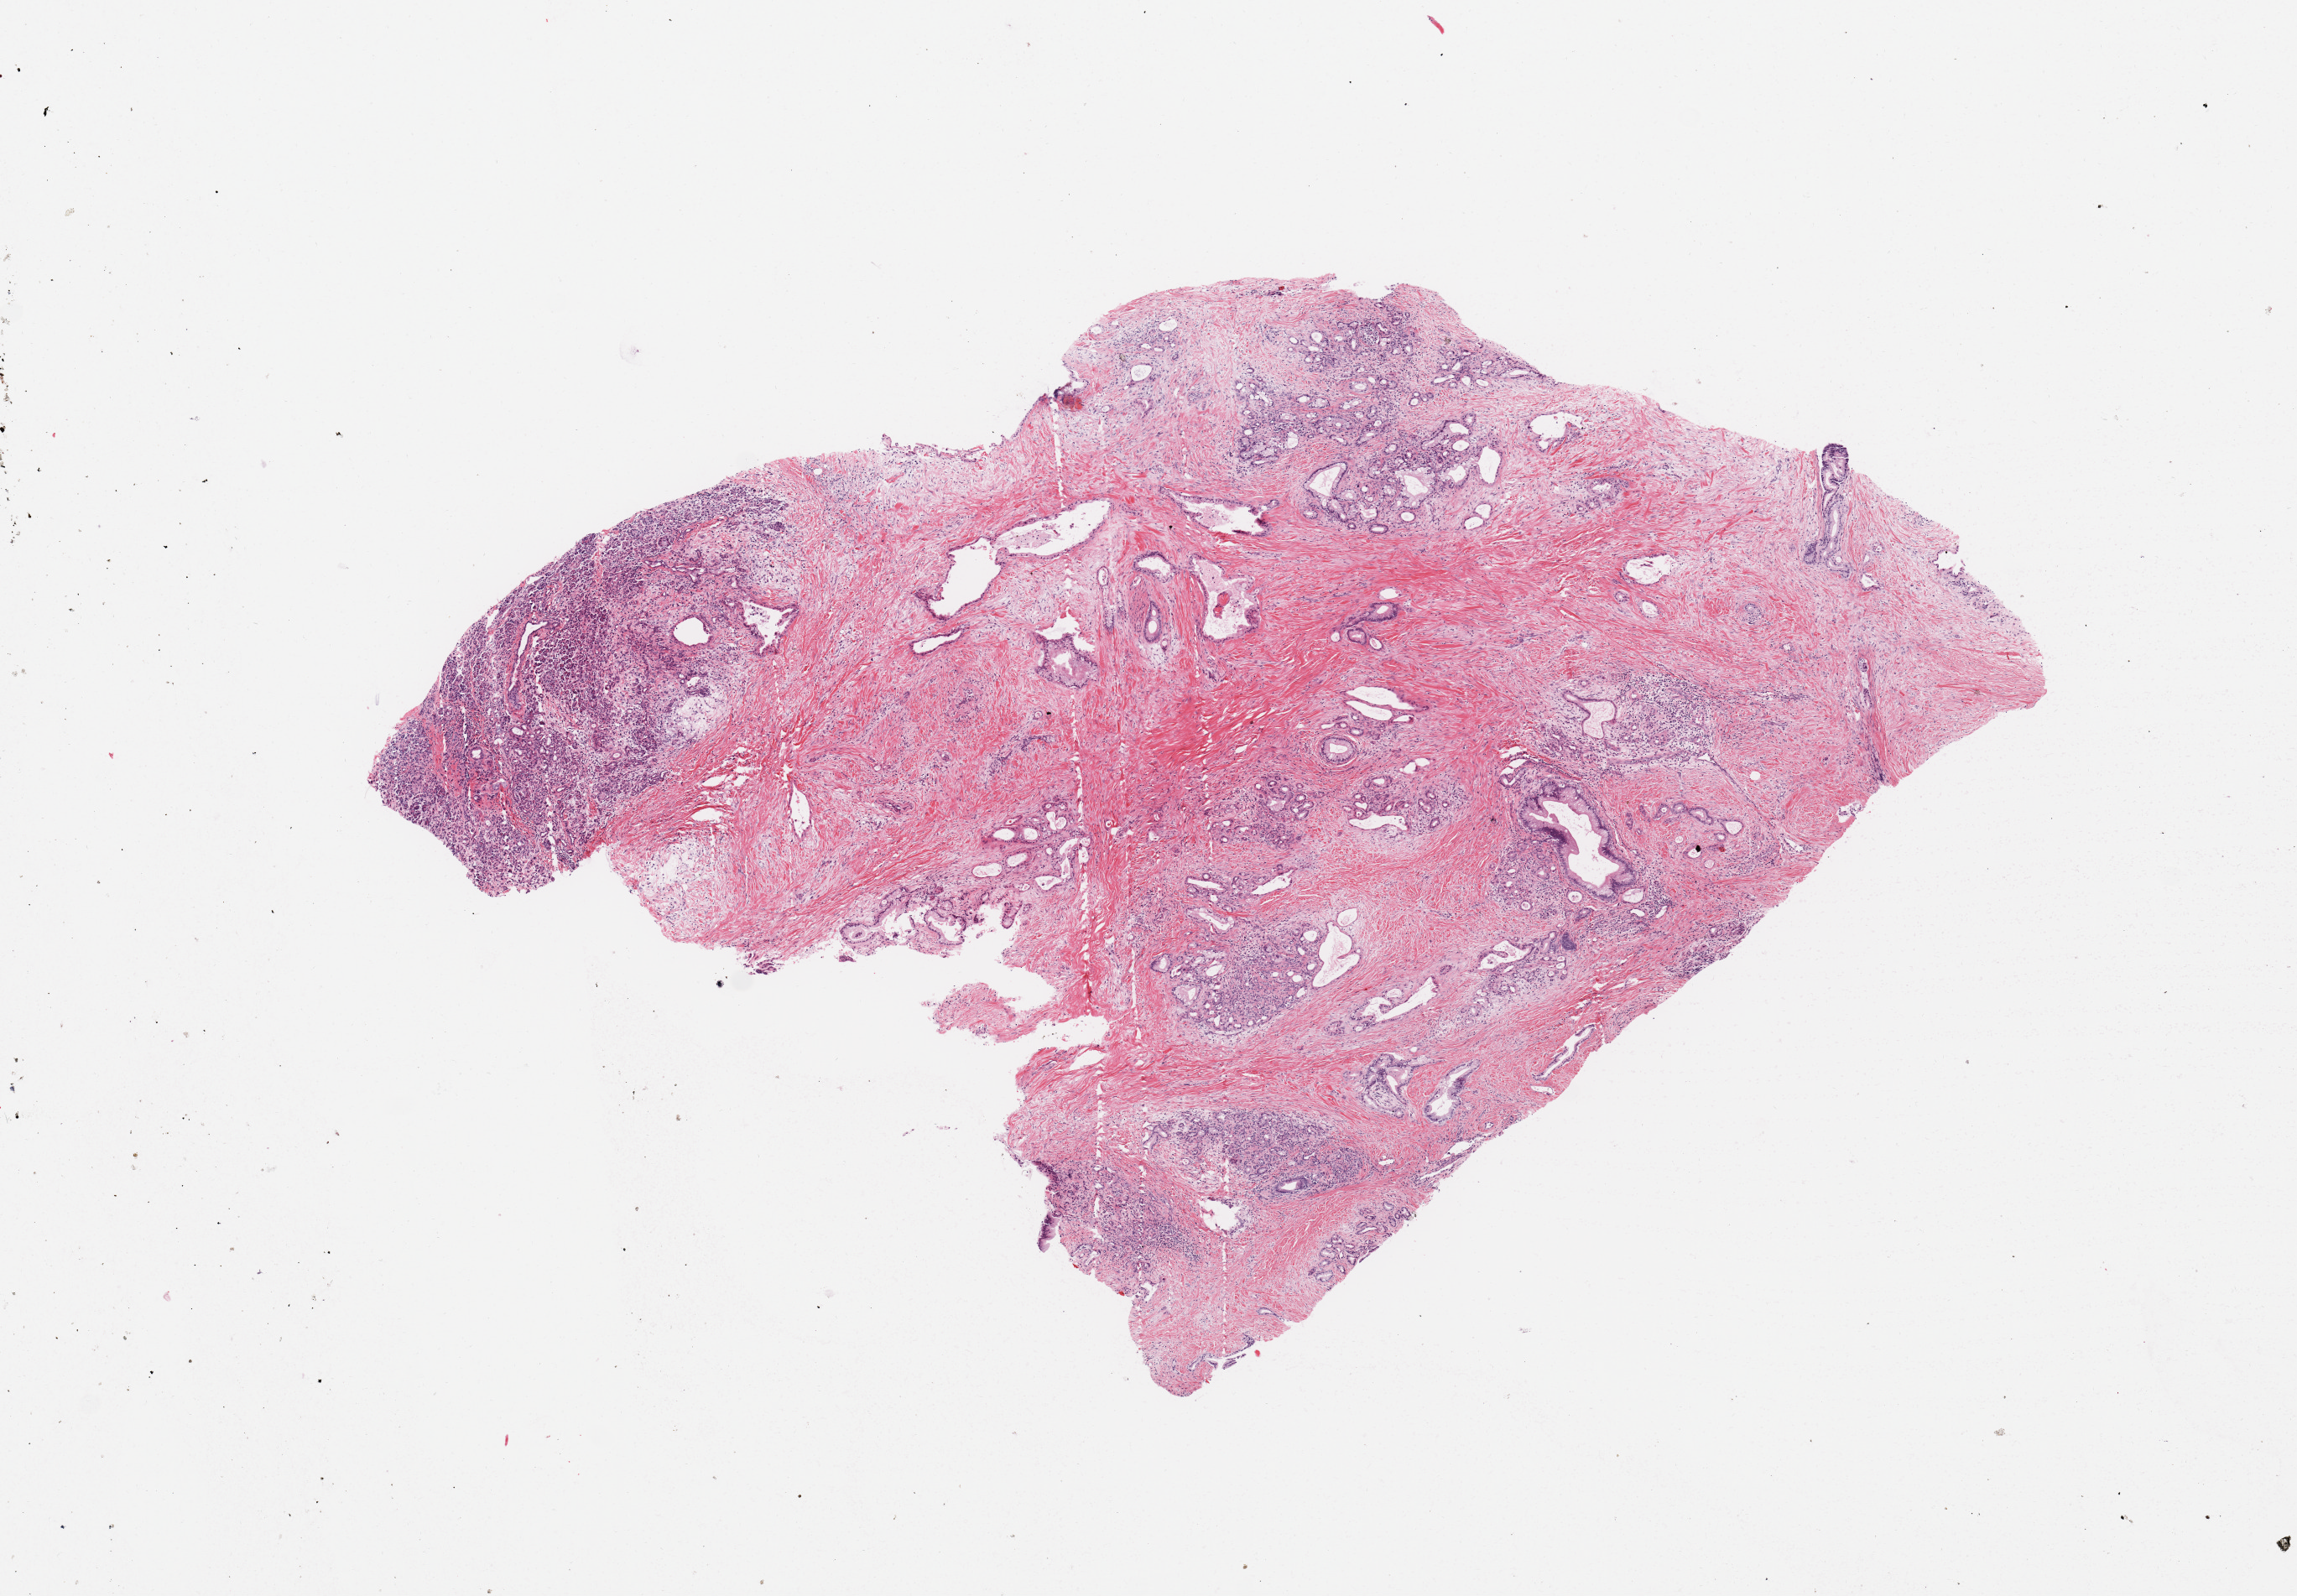
Hematoxylin and eosin (H&E) stained whole-slide image, a low-resolution overview of the entire scanned area, about 10.8 x 7.5 mm. Tumour tissue sample, sampled site: pancreas. 43-year-old male patient. Histologic grade: G2 (moderately differentiated). Pathologist review of this section (percent, as recorded): tumour nuclei 20%, necrosis 0%.
Primary tumour site (as recorded): head. Histologic diagnosis: Infiltrating duct carcinoma, NOS. AJCC pathologic stage: III.